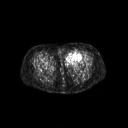
FDG PET of an extremity soft-tissue mass (from a PET/CT study), one axial slice; position 33 of 267 along the scan axis; 3.27 mm slice thickness; 128 × 128 image matrix, field of view 700 × 700 mm. Female patient, age 47 years. From the clinical record (not read from this slice): histological type: myxofibrosarcoma; grade: intermediate; site of the primary tumour: left thigh.
Structures marked on this image (expert contour drawn on MRI and transferred to this co-registered scan by the dataset authors):
- gross tumour volume including surrounding oedema: bounding box <65,51,83,66> (left, top, right, bottom; pixels)
- gross tumour volume (mass): <66,51,82,62>